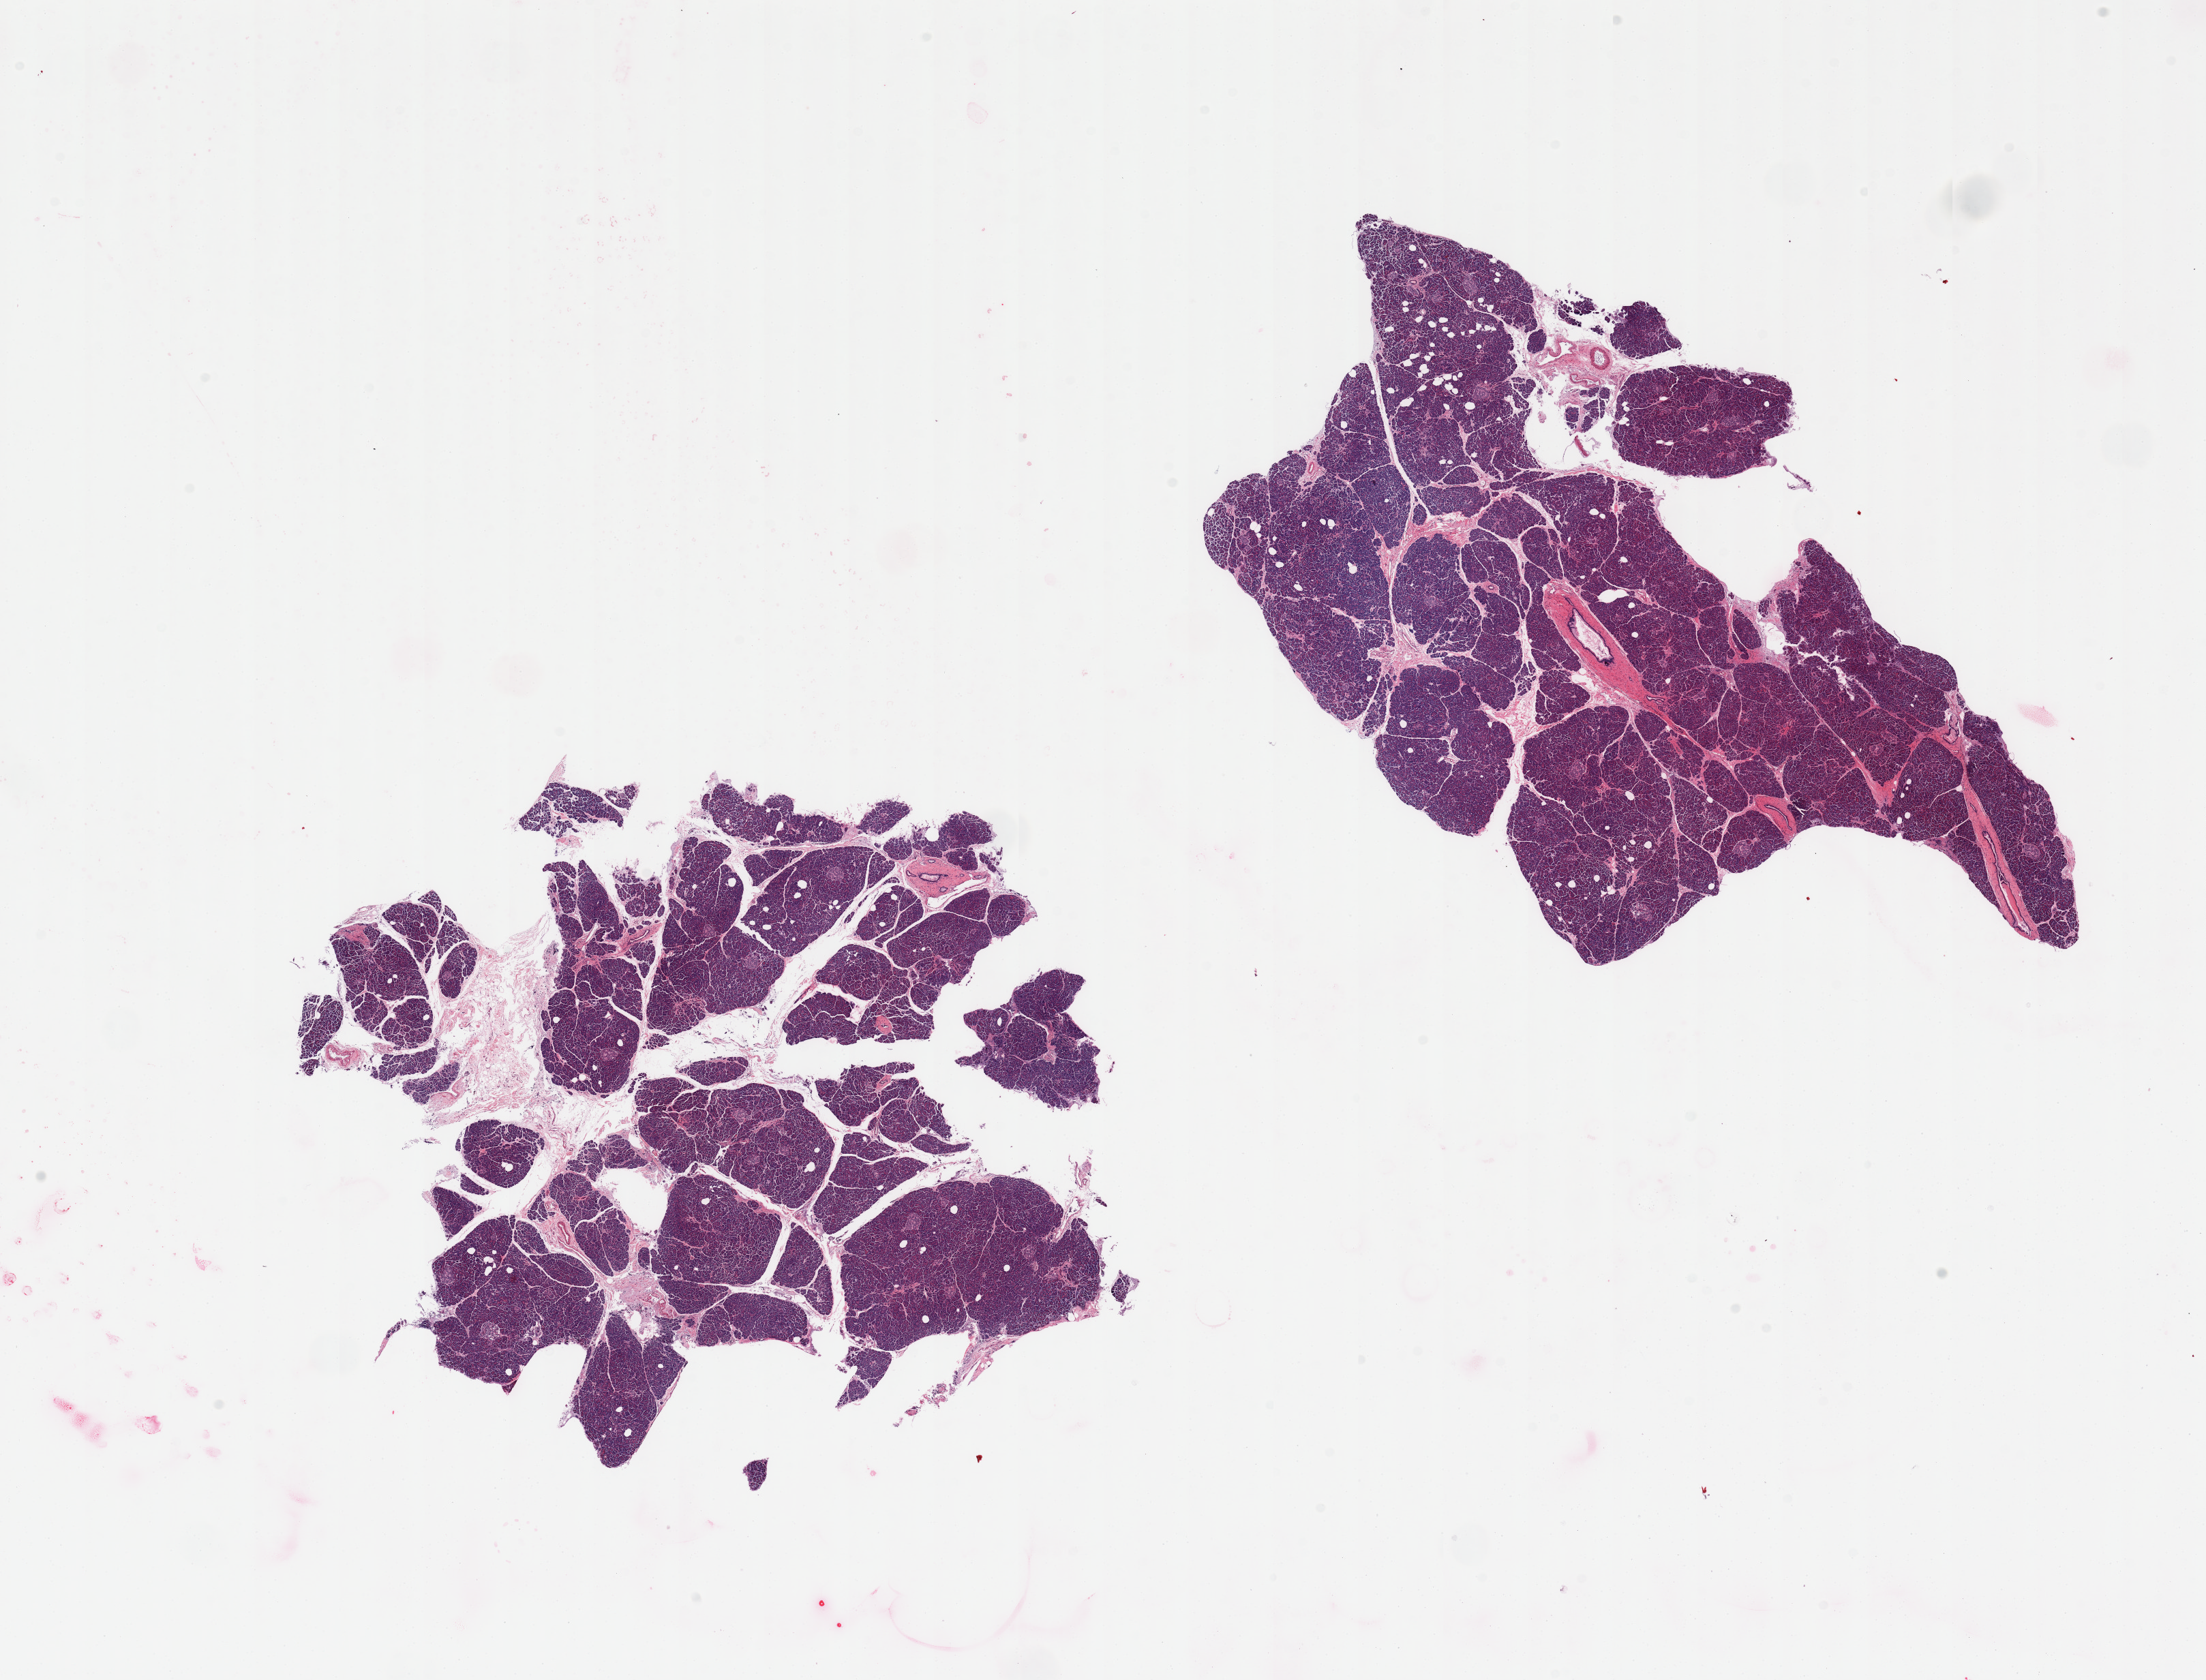
Digitized haematoxylin and eosin-stained section — a low-resolution overview of the entire scanned area, about 25.6 x 19.5 mm. PAXgene-fixed, paraffin-embedded tissue. Sampled site (target tissue): pancreas. Tissue donor sample.
- pathologist's review note for this sample: 2 pieces; one large duct with PanIN !a